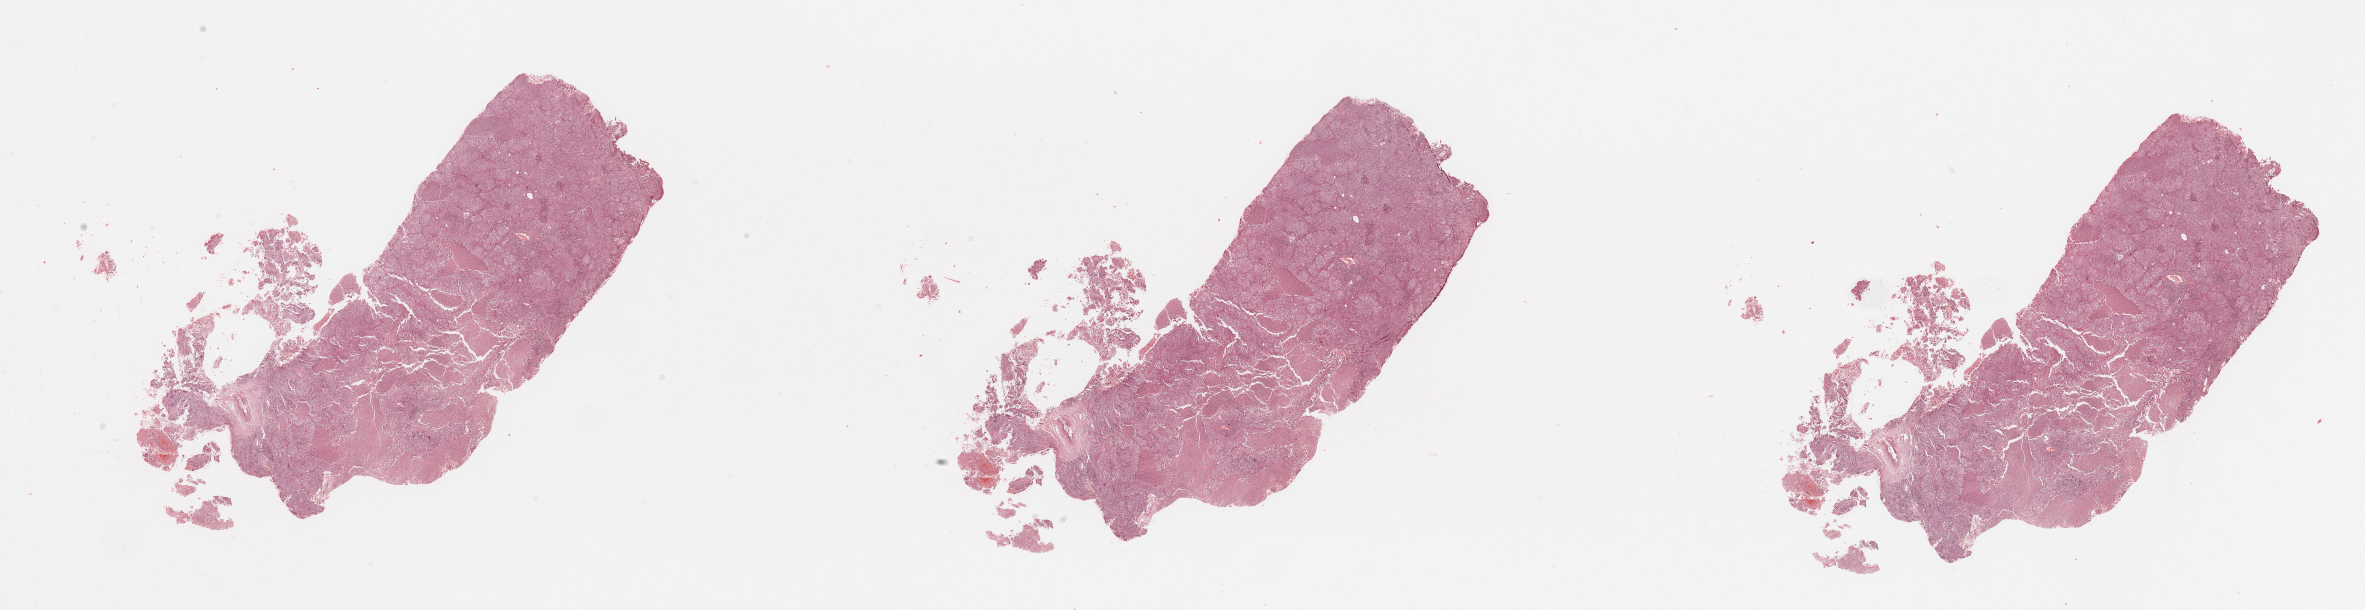
Whole-slide histology image, H&E-stained — whole scanned area (about 37.4 x 9.6 mm) shown as a low-resolution overview, tumour tissue sample, lung. 71-year-old male patient.
Patient diagnosis (cohort enrolment): squamous cell carcinoma (lung).